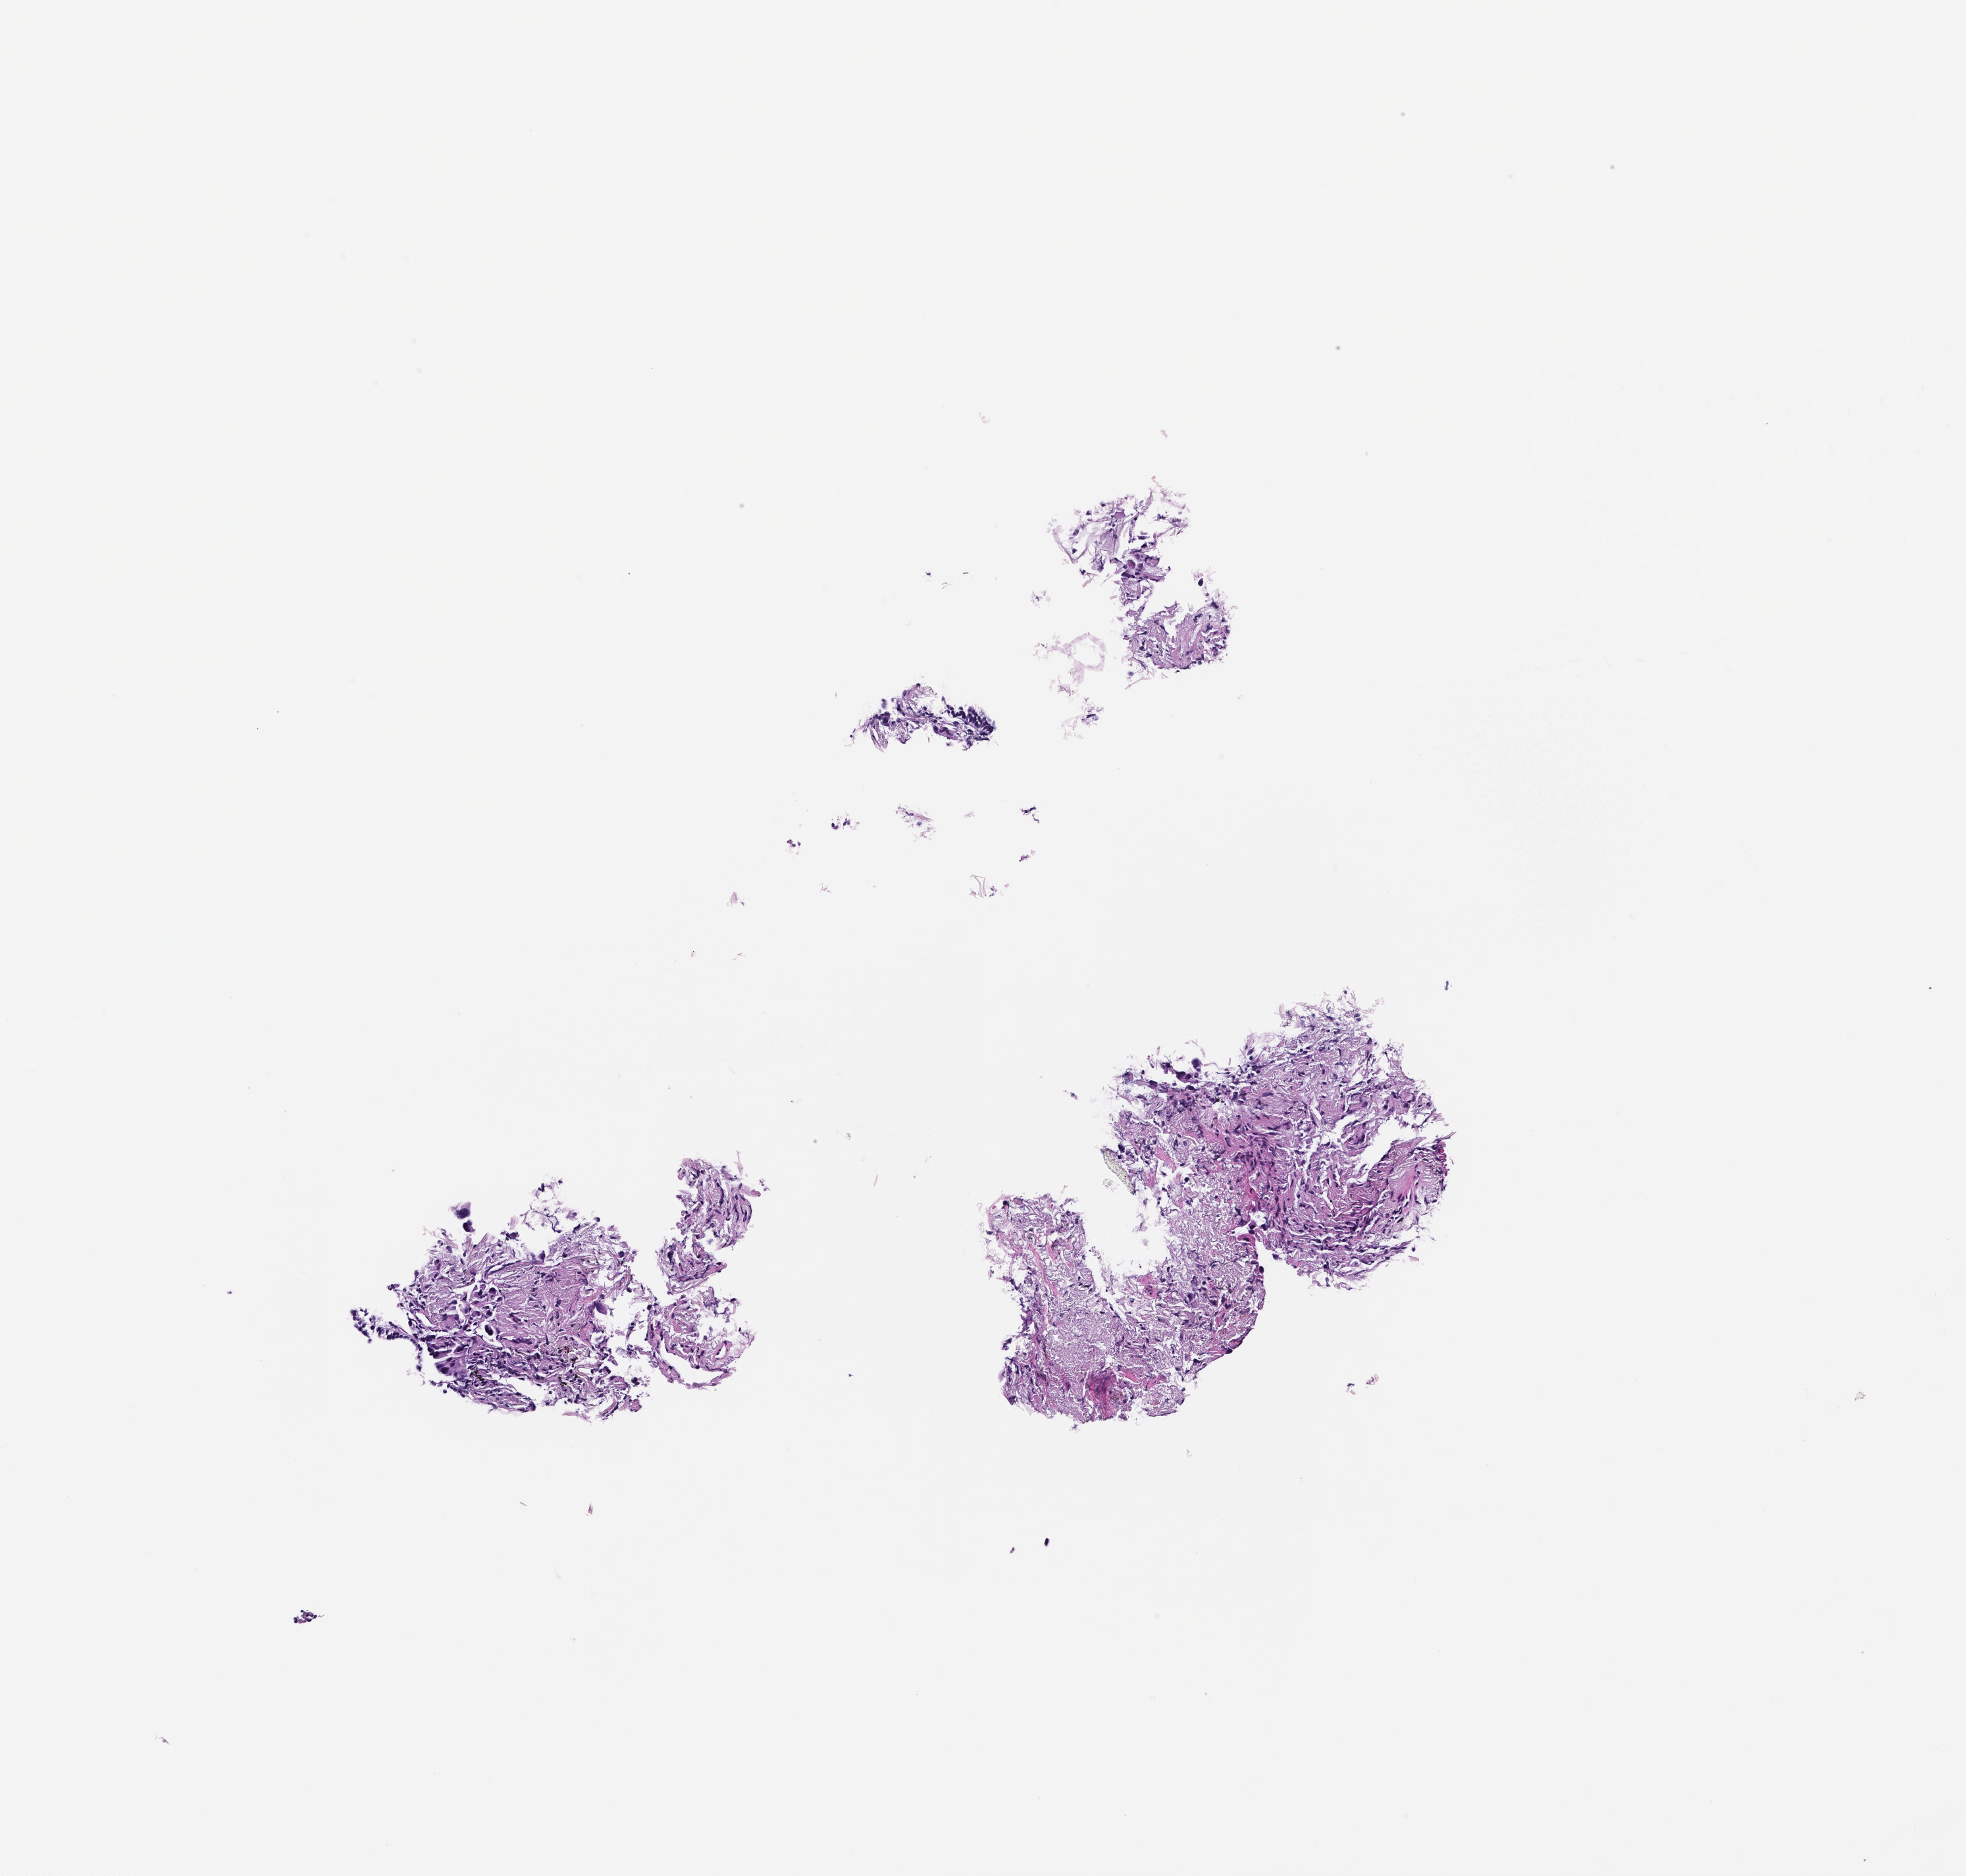
H&E whole-slide image — whole scanned area (about 3.0 x 2.9 mm) shown as a low-resolution overview. Formalin-fixed, paraffin-embedded (FFPE) tissue. Tissue site: lung. Patient sex: male.
* this section: primary tumour tissue
* diagnosis: Non-Small Cell Lung Carcinoma